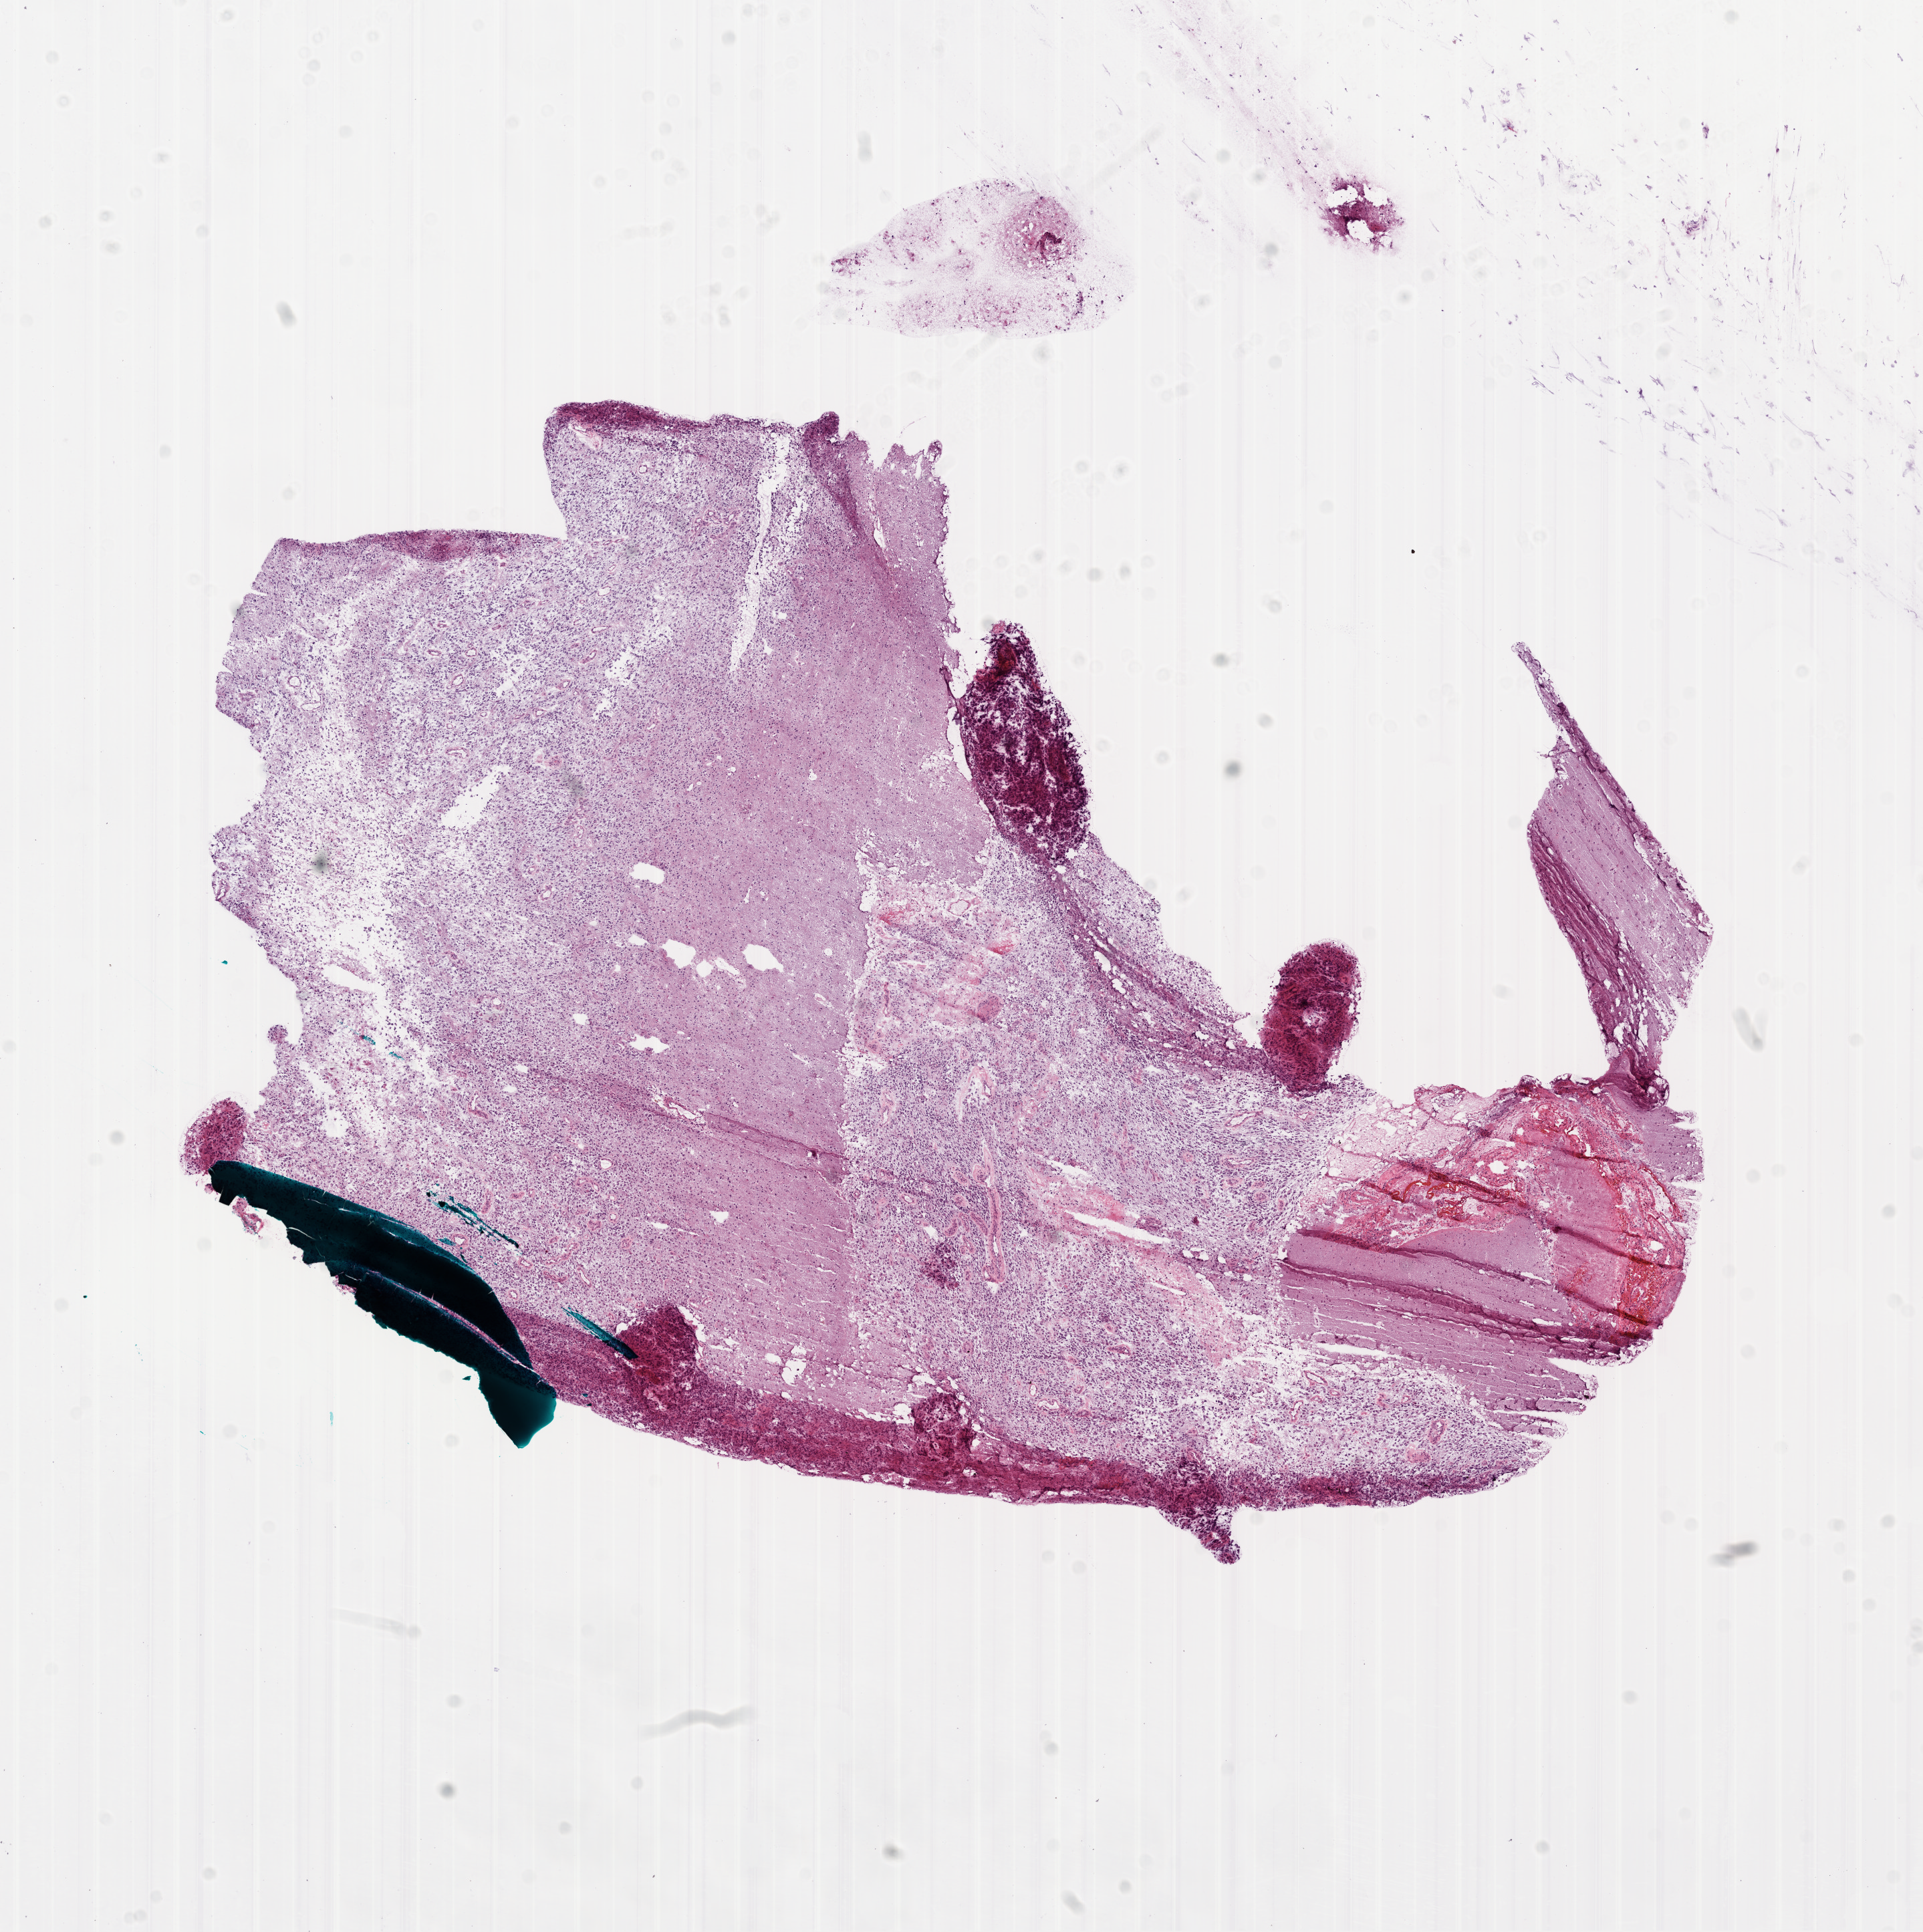
Whole-slide histology image, Hematoxylin and eosin (H&E) stained, a low-resolution overview of the entire scanned area, about 11.6 x 11.7 mm; frozen section; primary tumour sample from the brain. Male, age 53 years at initial diagnosis. Slide review estimates, as recorded: tumour cells 65%, tumour nuclei 90%, normal cells 30%, stromal cells 0%, necrosis 5%.
- histologic diagnosis: Glioblastoma